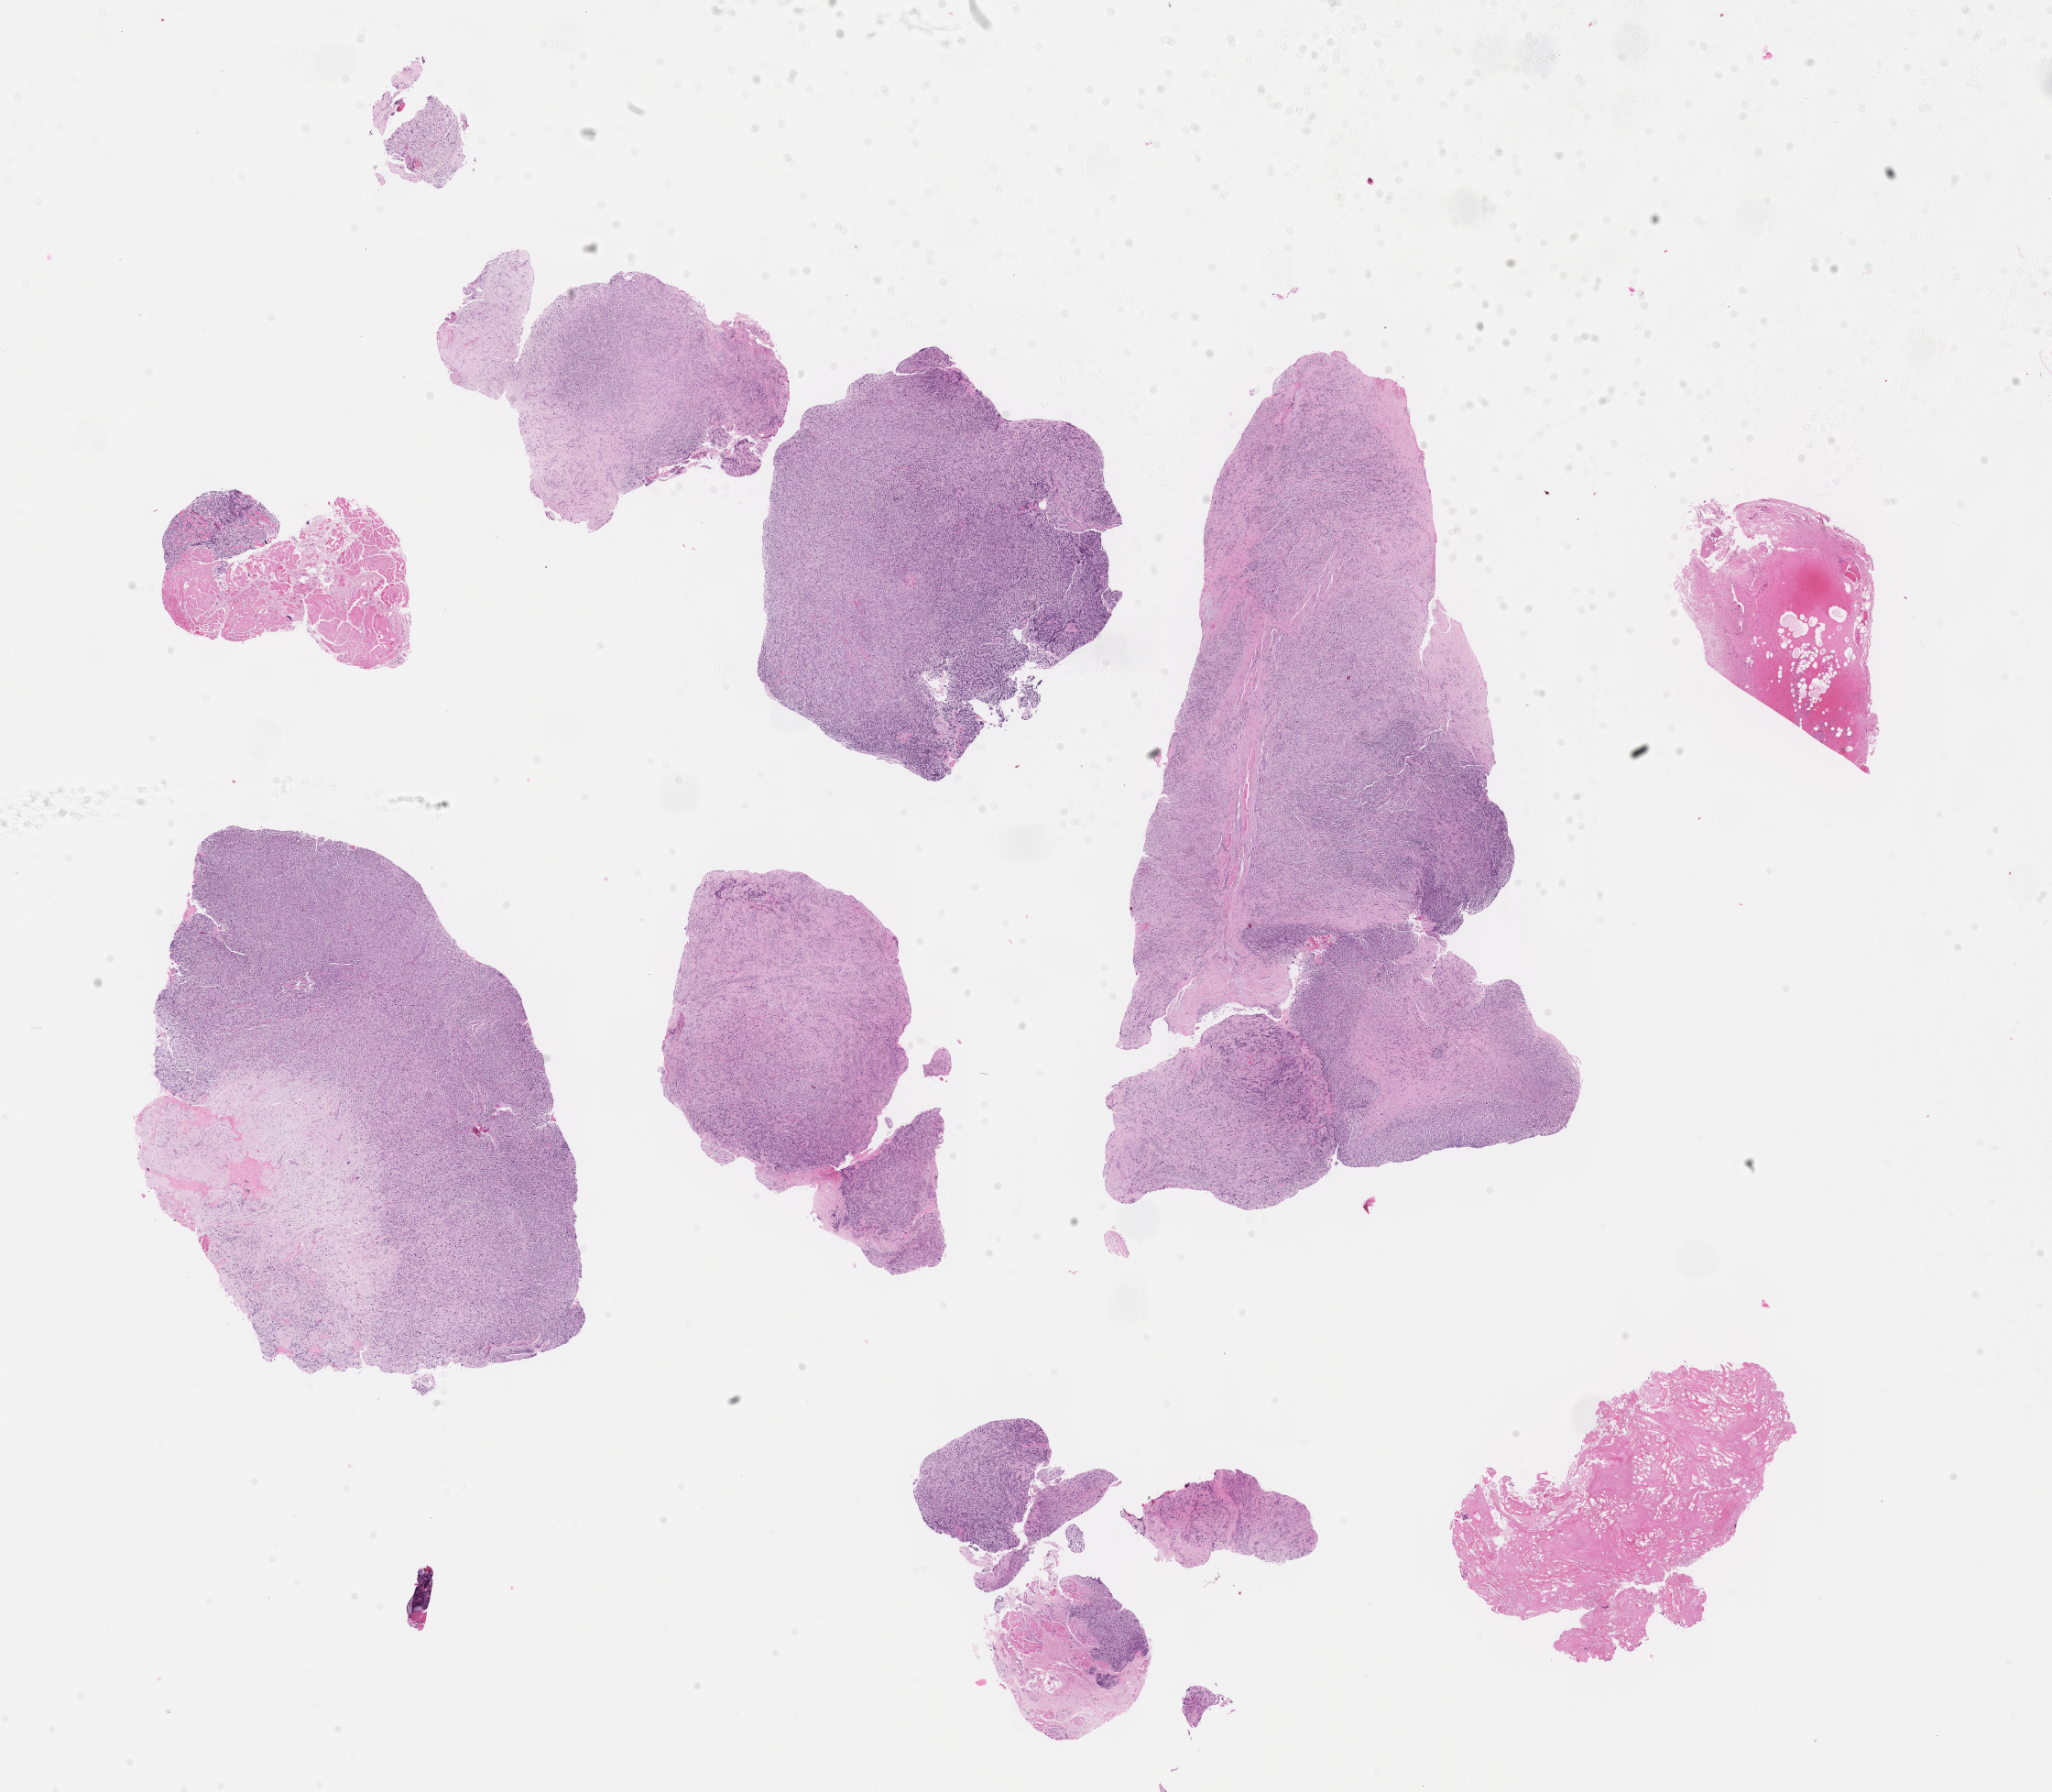
Whole-slide image, hematoxylin and eosin (H&E) stain of tumor tissue, whole scanned area (about 18.1 x 15.8 mm) shown as a low-resolution overview; FFPE section; site: nasal cavity-left. Patient: female, age 2.3 years at diagnosis.
- primary site (case record): nasal Cavity & Sinus
- diagnosis: rhabdomyosarcoma; histological classification: embryonal rhabdomyosarcoma
- stage (as recorded): 2
- metastatic status at presentation (as recorded): non-metastatic